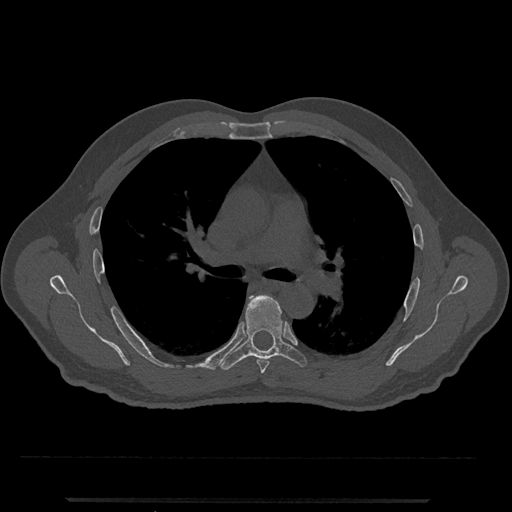
CT including the spine, one axial slice. Position 755 of 797 along the scan axis. Reconstruction kernel Br40s/3. 120 kVp. Bone window (W 1800 / L 400 HU). 0.5 mm slice thickness. 512 × 512 image matrix. Male patient, age 63 years. From the clinical record (not read from this slice): primary cancer: prostate.
Structures marked on this image (semi-automatically segmented with operator editing):
- T5 vertebra: bounding box <257,359,270,374> (left, top, right, bottom; pixels)
- T6 vertebra: <219,294,307,371>